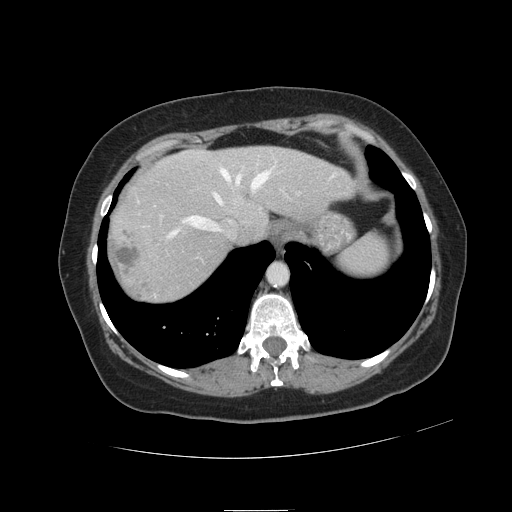
Contrast-enhanced abdominal CT, one axial slice. Position 98 of 121 along the scan axis. 120 kVp. Intravenous contrast given. Soft-tissue window (W 400 / L 40 HU). 2.5 mm slice thickness. 512 × 512 image matrix. Female patient, age 52 years. From the clinical record (not read from this slice): diagnosis: colorectal cancer liver metastases, imaged before liver resection; multiple liver metastases: yes; largest metastasis: 6.3 cm; disease in both lobes: no.
Structures marked on this image (manually delineated by an expert):
- hepatic veins: bounding box [x1, y1, x2, y2] px = [138, 168, 269, 238]
- liver: [108, 147, 351, 303]
- planned liver remnant (the part of the liver to remain after resection): [170, 147, 352, 243]
- liver metastasis: [114, 246, 139, 274]